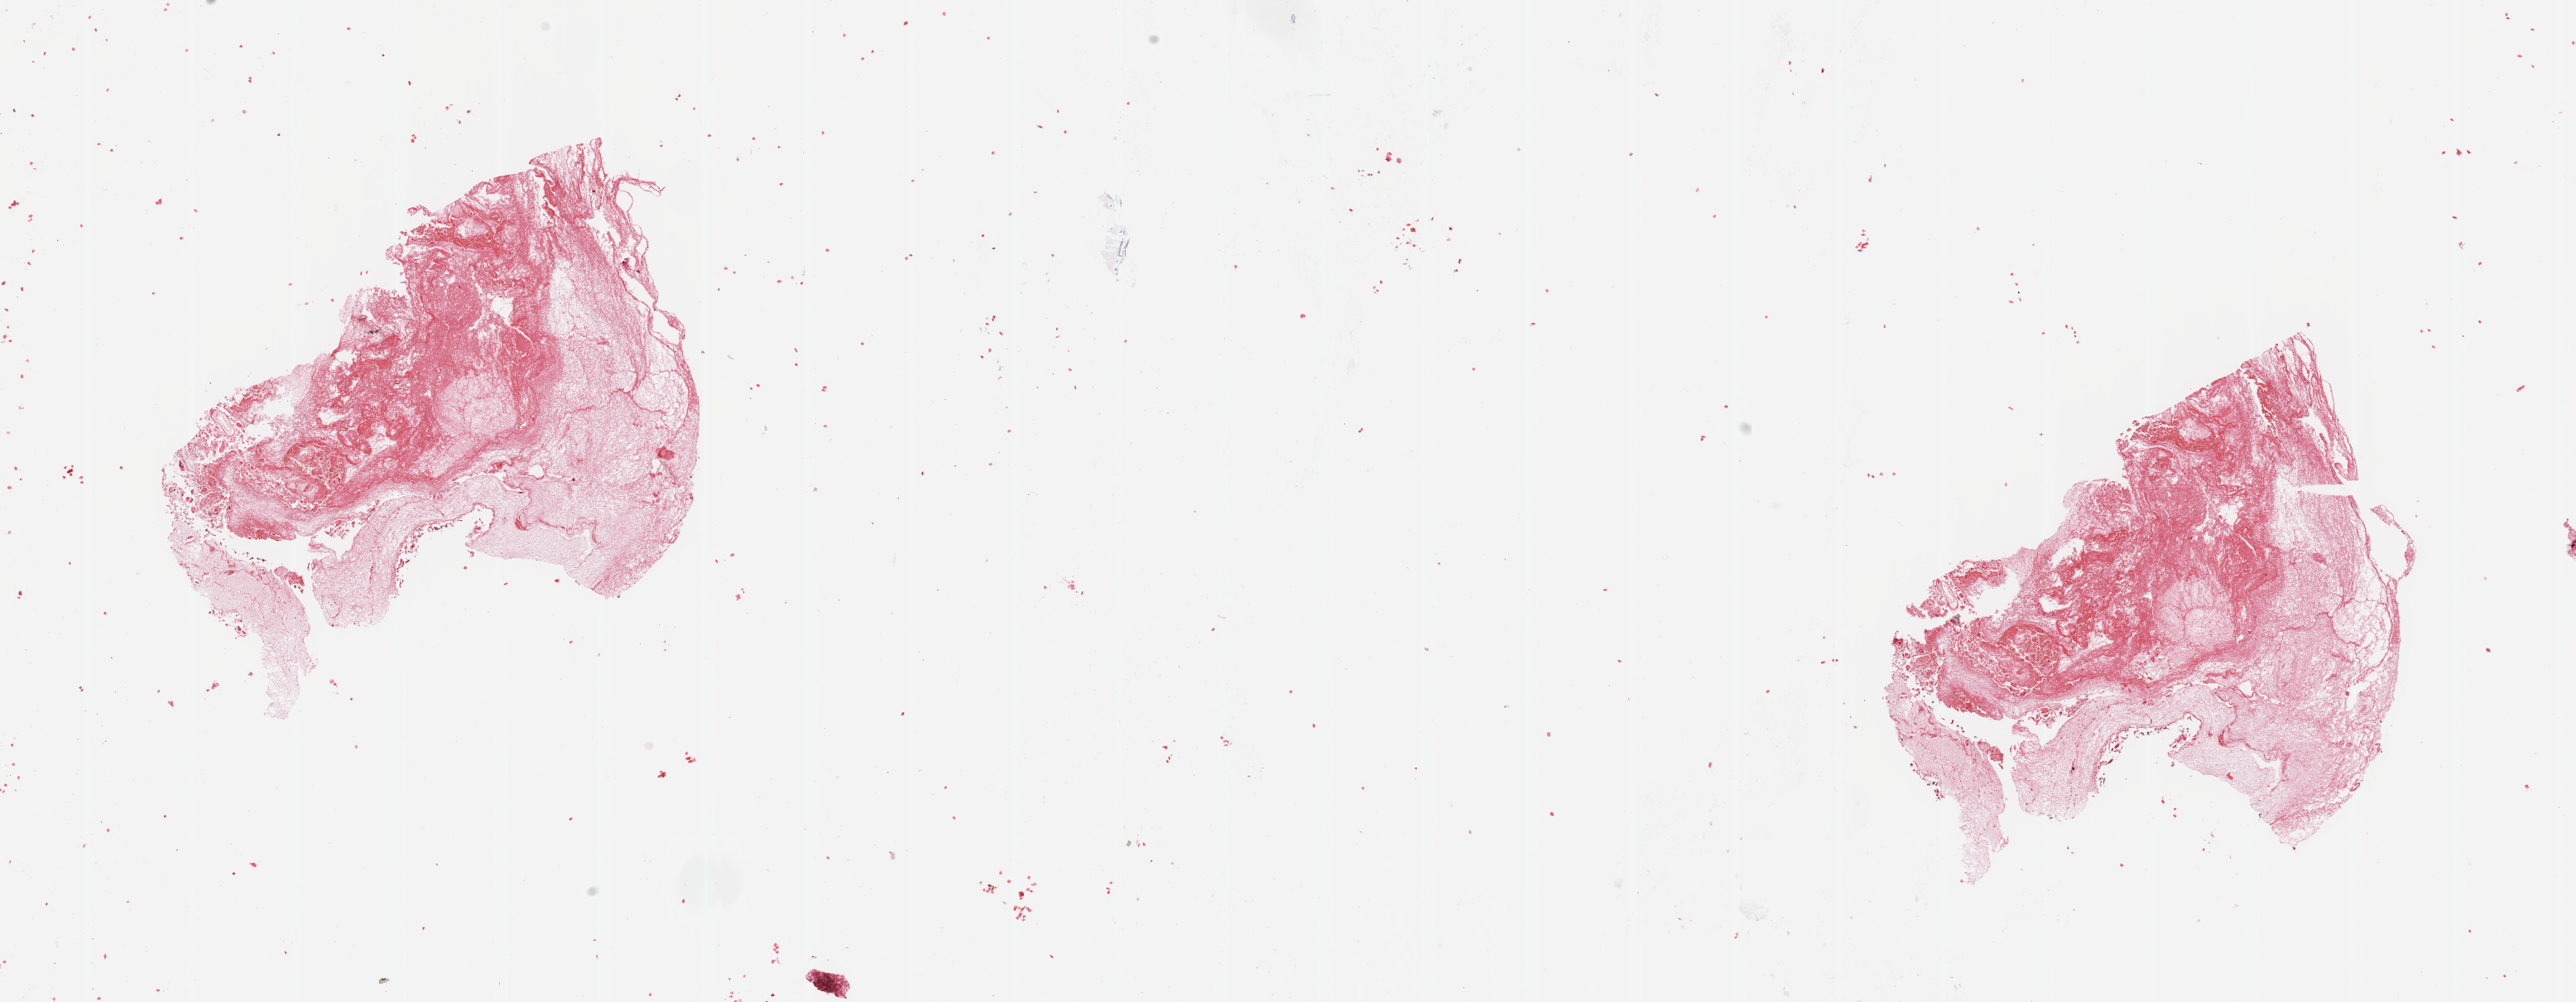
Whole-slide histology image, Hematoxylin and eosin (H&E) stained, a low-resolution overview of the entire scanned area, about 24.6 x 9.6 mm (slide scanned at 20x), brain, tumour tissue. Patient: male, age 39 years.
Primary tumour site (as recorded): frontal lobe. Histologic diagnosis: Glioblastoma.